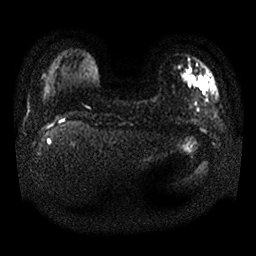
Breast MRI, one axial slice; position 3 of 25 along the scan axis; diffusion-weighted series; image 2 of 4 stored at this slice position (different b-values; order by instance number); 1.5 T; 4 mm slice thickness; 256 × 256 image matrix, field of view 340 × 340 mm. Female patient.
Outlined on this slice (expert manual segmentation):
- tumour on diffusion-weighted imaging: box from (x=198, y=76) to (x=209, y=97) px